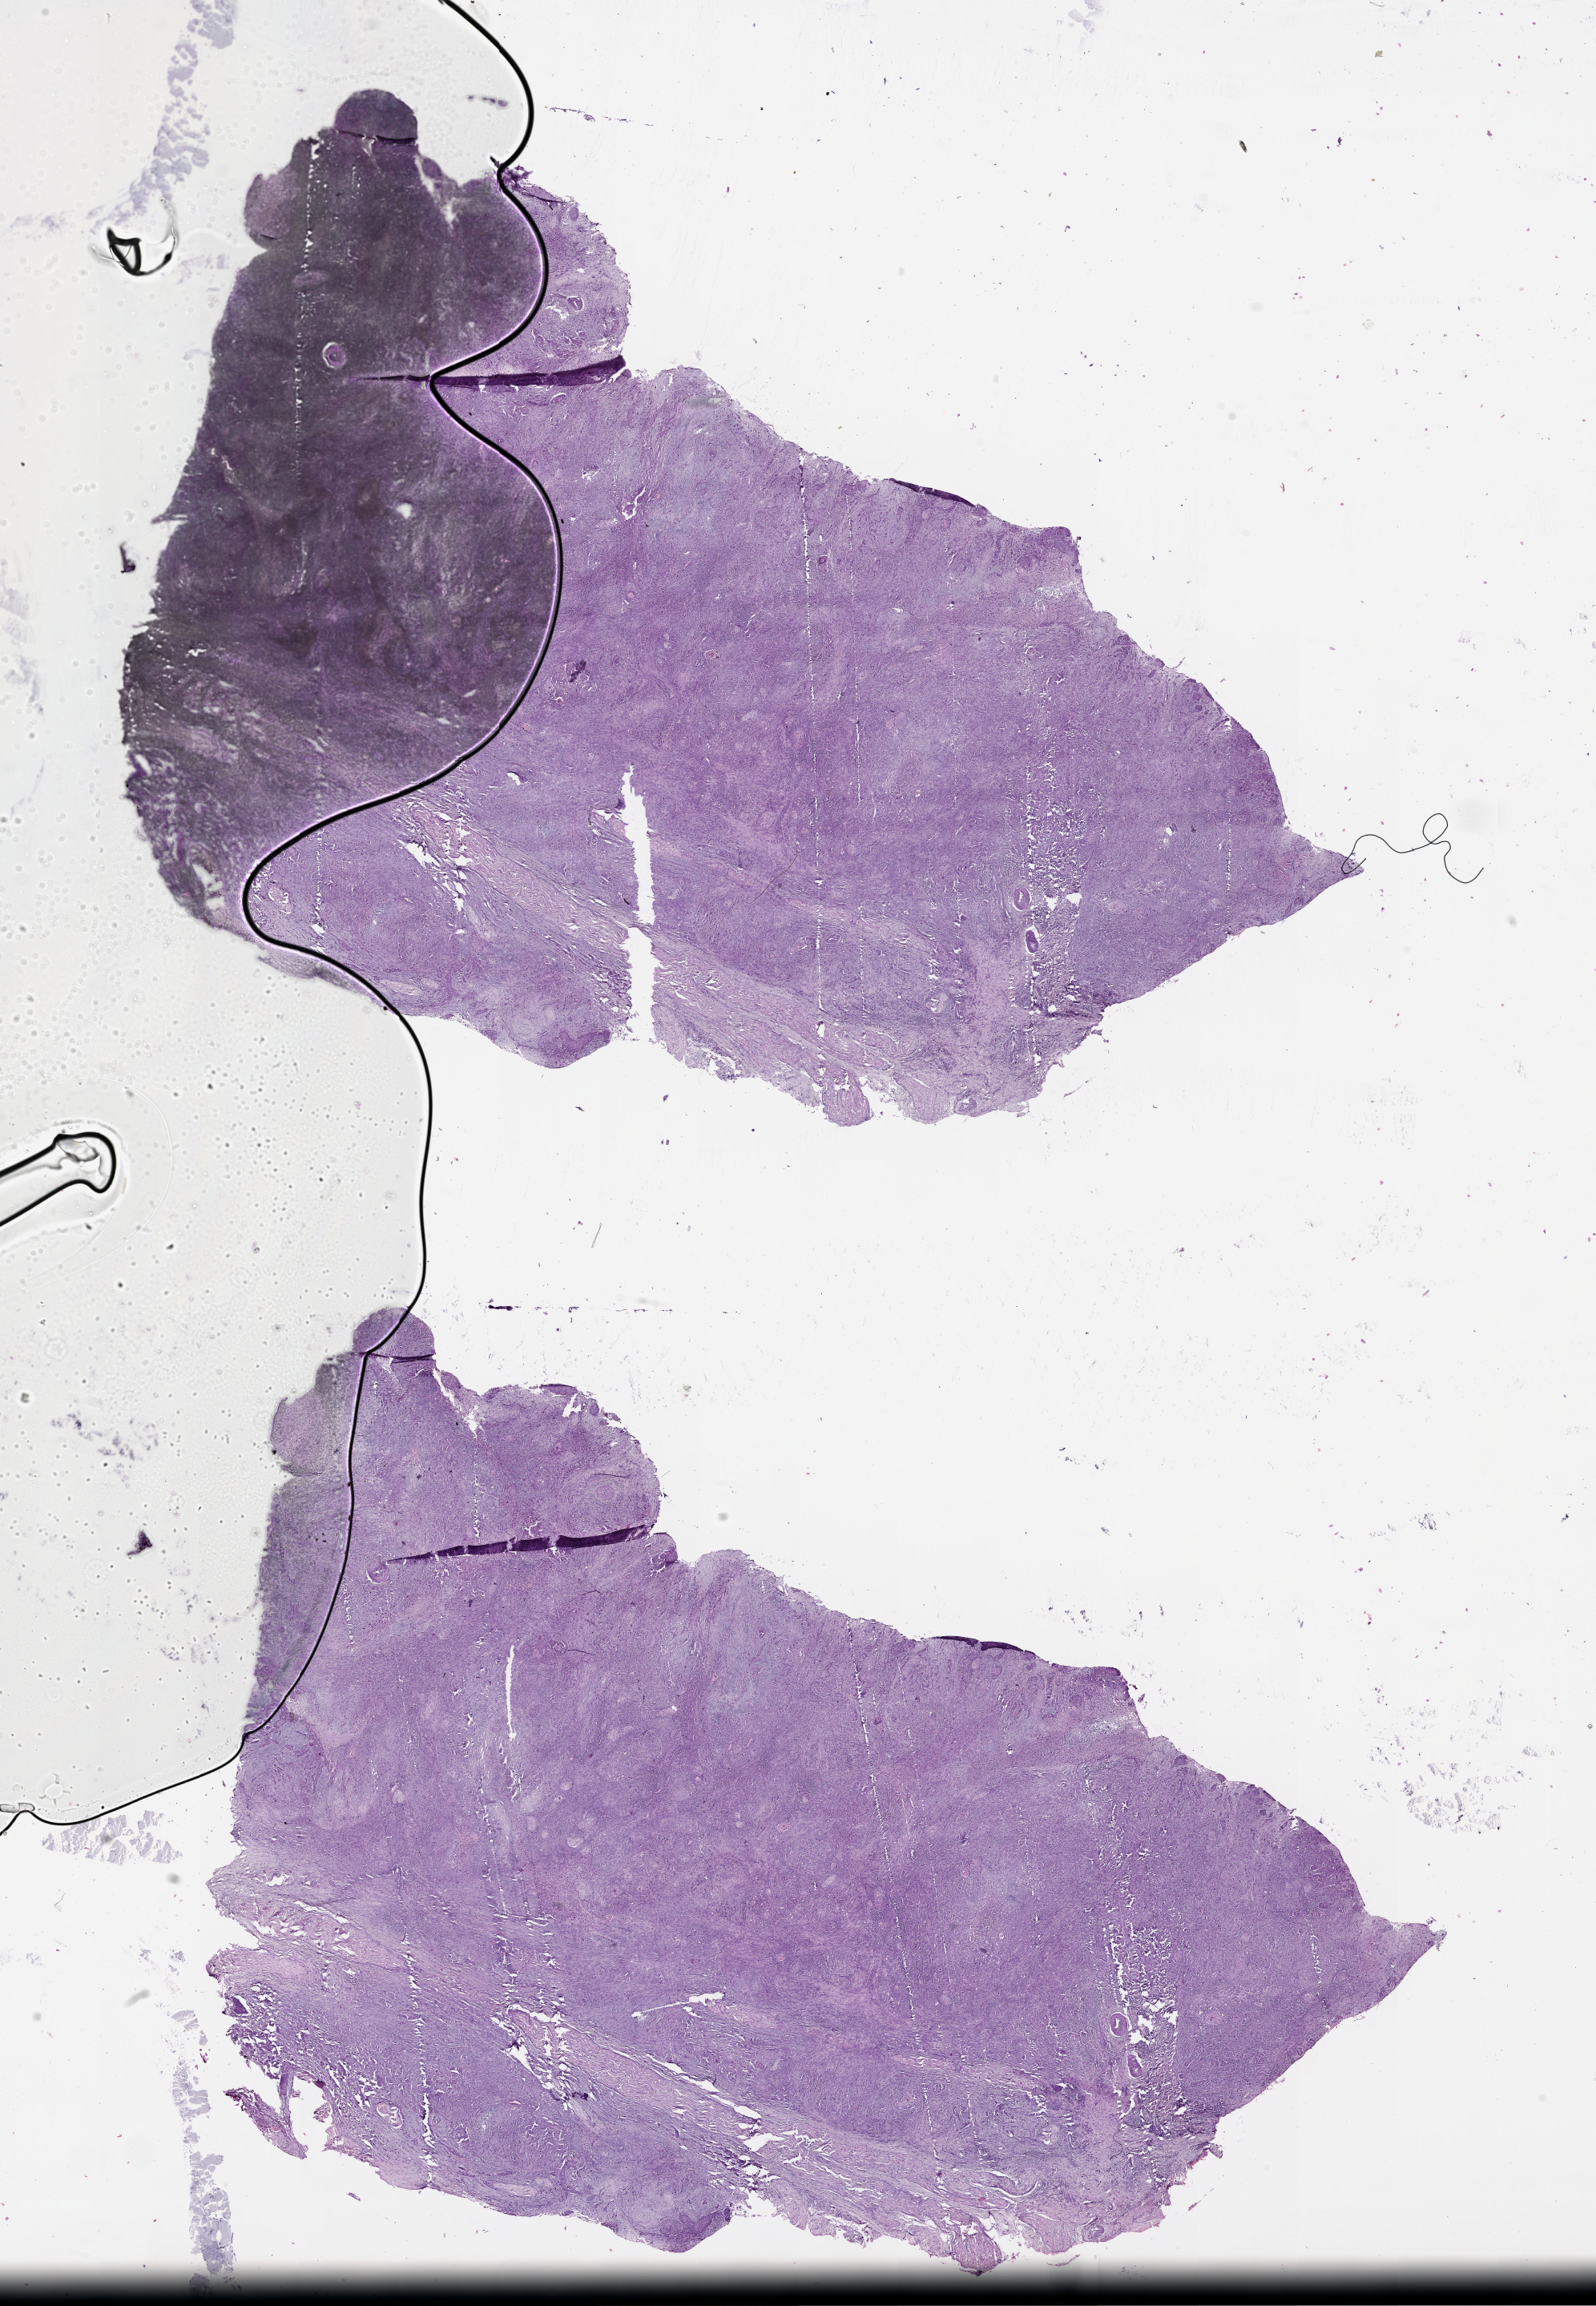
Whole-slide histology image, Hematoxylin and eosin (H&E) stained — whole scanned area (about 16.0 x 23.2 mm, from a 20x scan) shown as a low-resolution overview, head and neck, tissue type not recorded.
Patient diagnosis (cohort enrolment): head and neck cancer (head-neck).